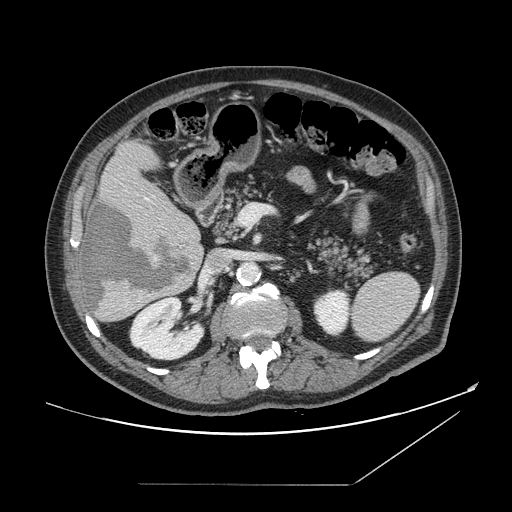
Contrast-enhanced abdominal CT, one axial slice; slice 77 of 166 in the series (ordered by position); 120 kVp; intravenous contrast given; soft-tissue window (W 400 / L 40 HU); 2.5 mm slice thickness; 512 × 512 image matrix, field of view 416 × 416 mm. Male patient, age 80 years. Case-level facts recorded for this patient, not image findings: diagnosis: colorectal cancer liver metastases, imaged before liver resection; multiple liver metastases: no.
Annotated regions visible in this slice (outlined manually by an expert reader):
- hepatic veins: bounding box (x1, y1, x2, y2) in pixels: (147, 199, 149, 201)
- liver: (79, 142, 205, 324)
- planned liver remnant (the part of the liver to remain after resection): (102, 142, 197, 231)
- liver metastasis: (84, 200, 192, 311)